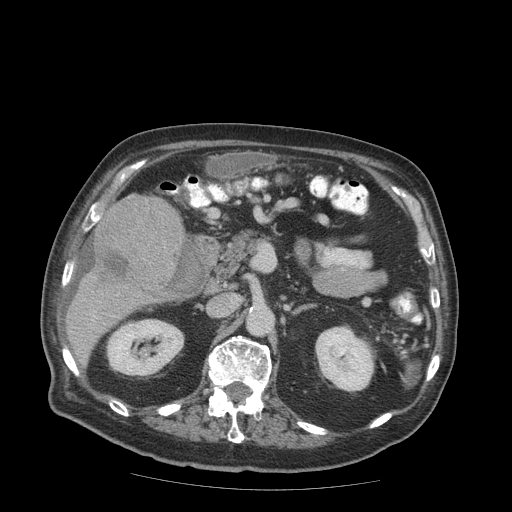
Contrast-enhanced abdominal CT (liver protocol), one axial slice; position 34 of 99 along the scan axis; 140 kVp; soft-tissue window (W 400 / L 40 HU); 2.5 mm slice thickness; 512 × 512 image matrix, field of view 420 × 420 mm. From the clinical record (not read from this slice): diagnosis: hepatocellular carcinoma (patient treated with transarterial chemoembolisation; whether this scan precedes or follows treatment is not stated here); TNM stage (as recorded): Stage-IIIB; Child-Pugh class: A; tumour differentiation: well differentiated; tumour nodularity: multinodular.
Annotated regions visible in this slice (semi-automatically segmented with operator editing):
- liver parenchyma outside the tumour (the mass and vessels are separate outlines, so this box may not span the whole liver): bounding box [x1, y1, x2, y2] px = [66, 194, 186, 352]
- mass: [93, 192, 186, 291]